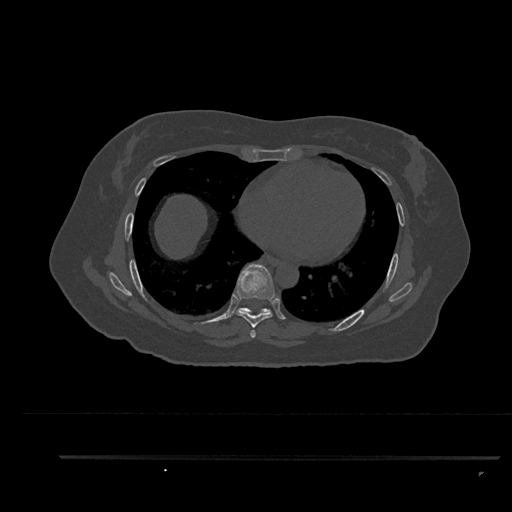
CT including the spine, one axial slice. Position 496 of 797 along the scan axis. Reconstruction kernel Br40s/3. 120 kVp. Bone window (W 1800 / L 400 HU). 0.5 mm slice thickness. 512 × 512 image matrix. Female patient, age 44 years. Case-level facts recorded for this patient, not image findings: primary cancer: renal.
Outlined on this slice (semi-automatically segmented with operator editing):
- T6 vertebra: box from (x=252, y=334) to (x=255, y=337) px
- T7 vertebra: (x=236, y=264)–(x=275, y=338)
- T8 vertebra: (x=237, y=308)–(x=271, y=315)